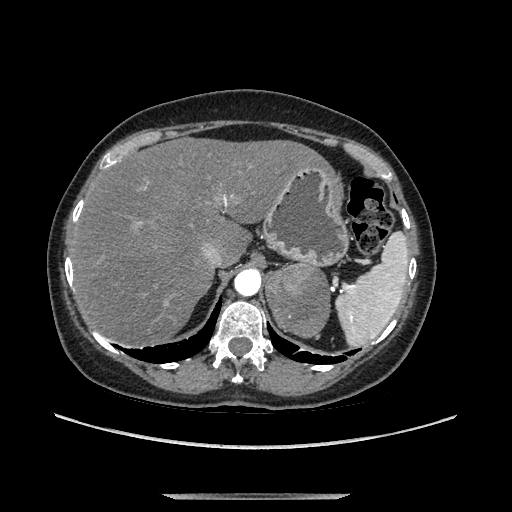
Contrast-enhanced abdominal CT, one axial slice. Position 100 of 169 along the scan axis. Soft-tissue window (W 400 / L 40 HU). 512 × 512 image matrix, field of view 400 × 400 mm. Female patient. Case-level facts recorded for this patient, not image findings: diagnosis: adrenocortical carcinoma; tumour side: left adrenal; tumour size at pathology: 9 cm; Ki-67 index: 2 %; stage (as recorded): 3.
Outlined on this slice (semi-automatically segmented with operator editing):
- mass: bounding box <268,267,327,337> (left, top, right, bottom; pixels)